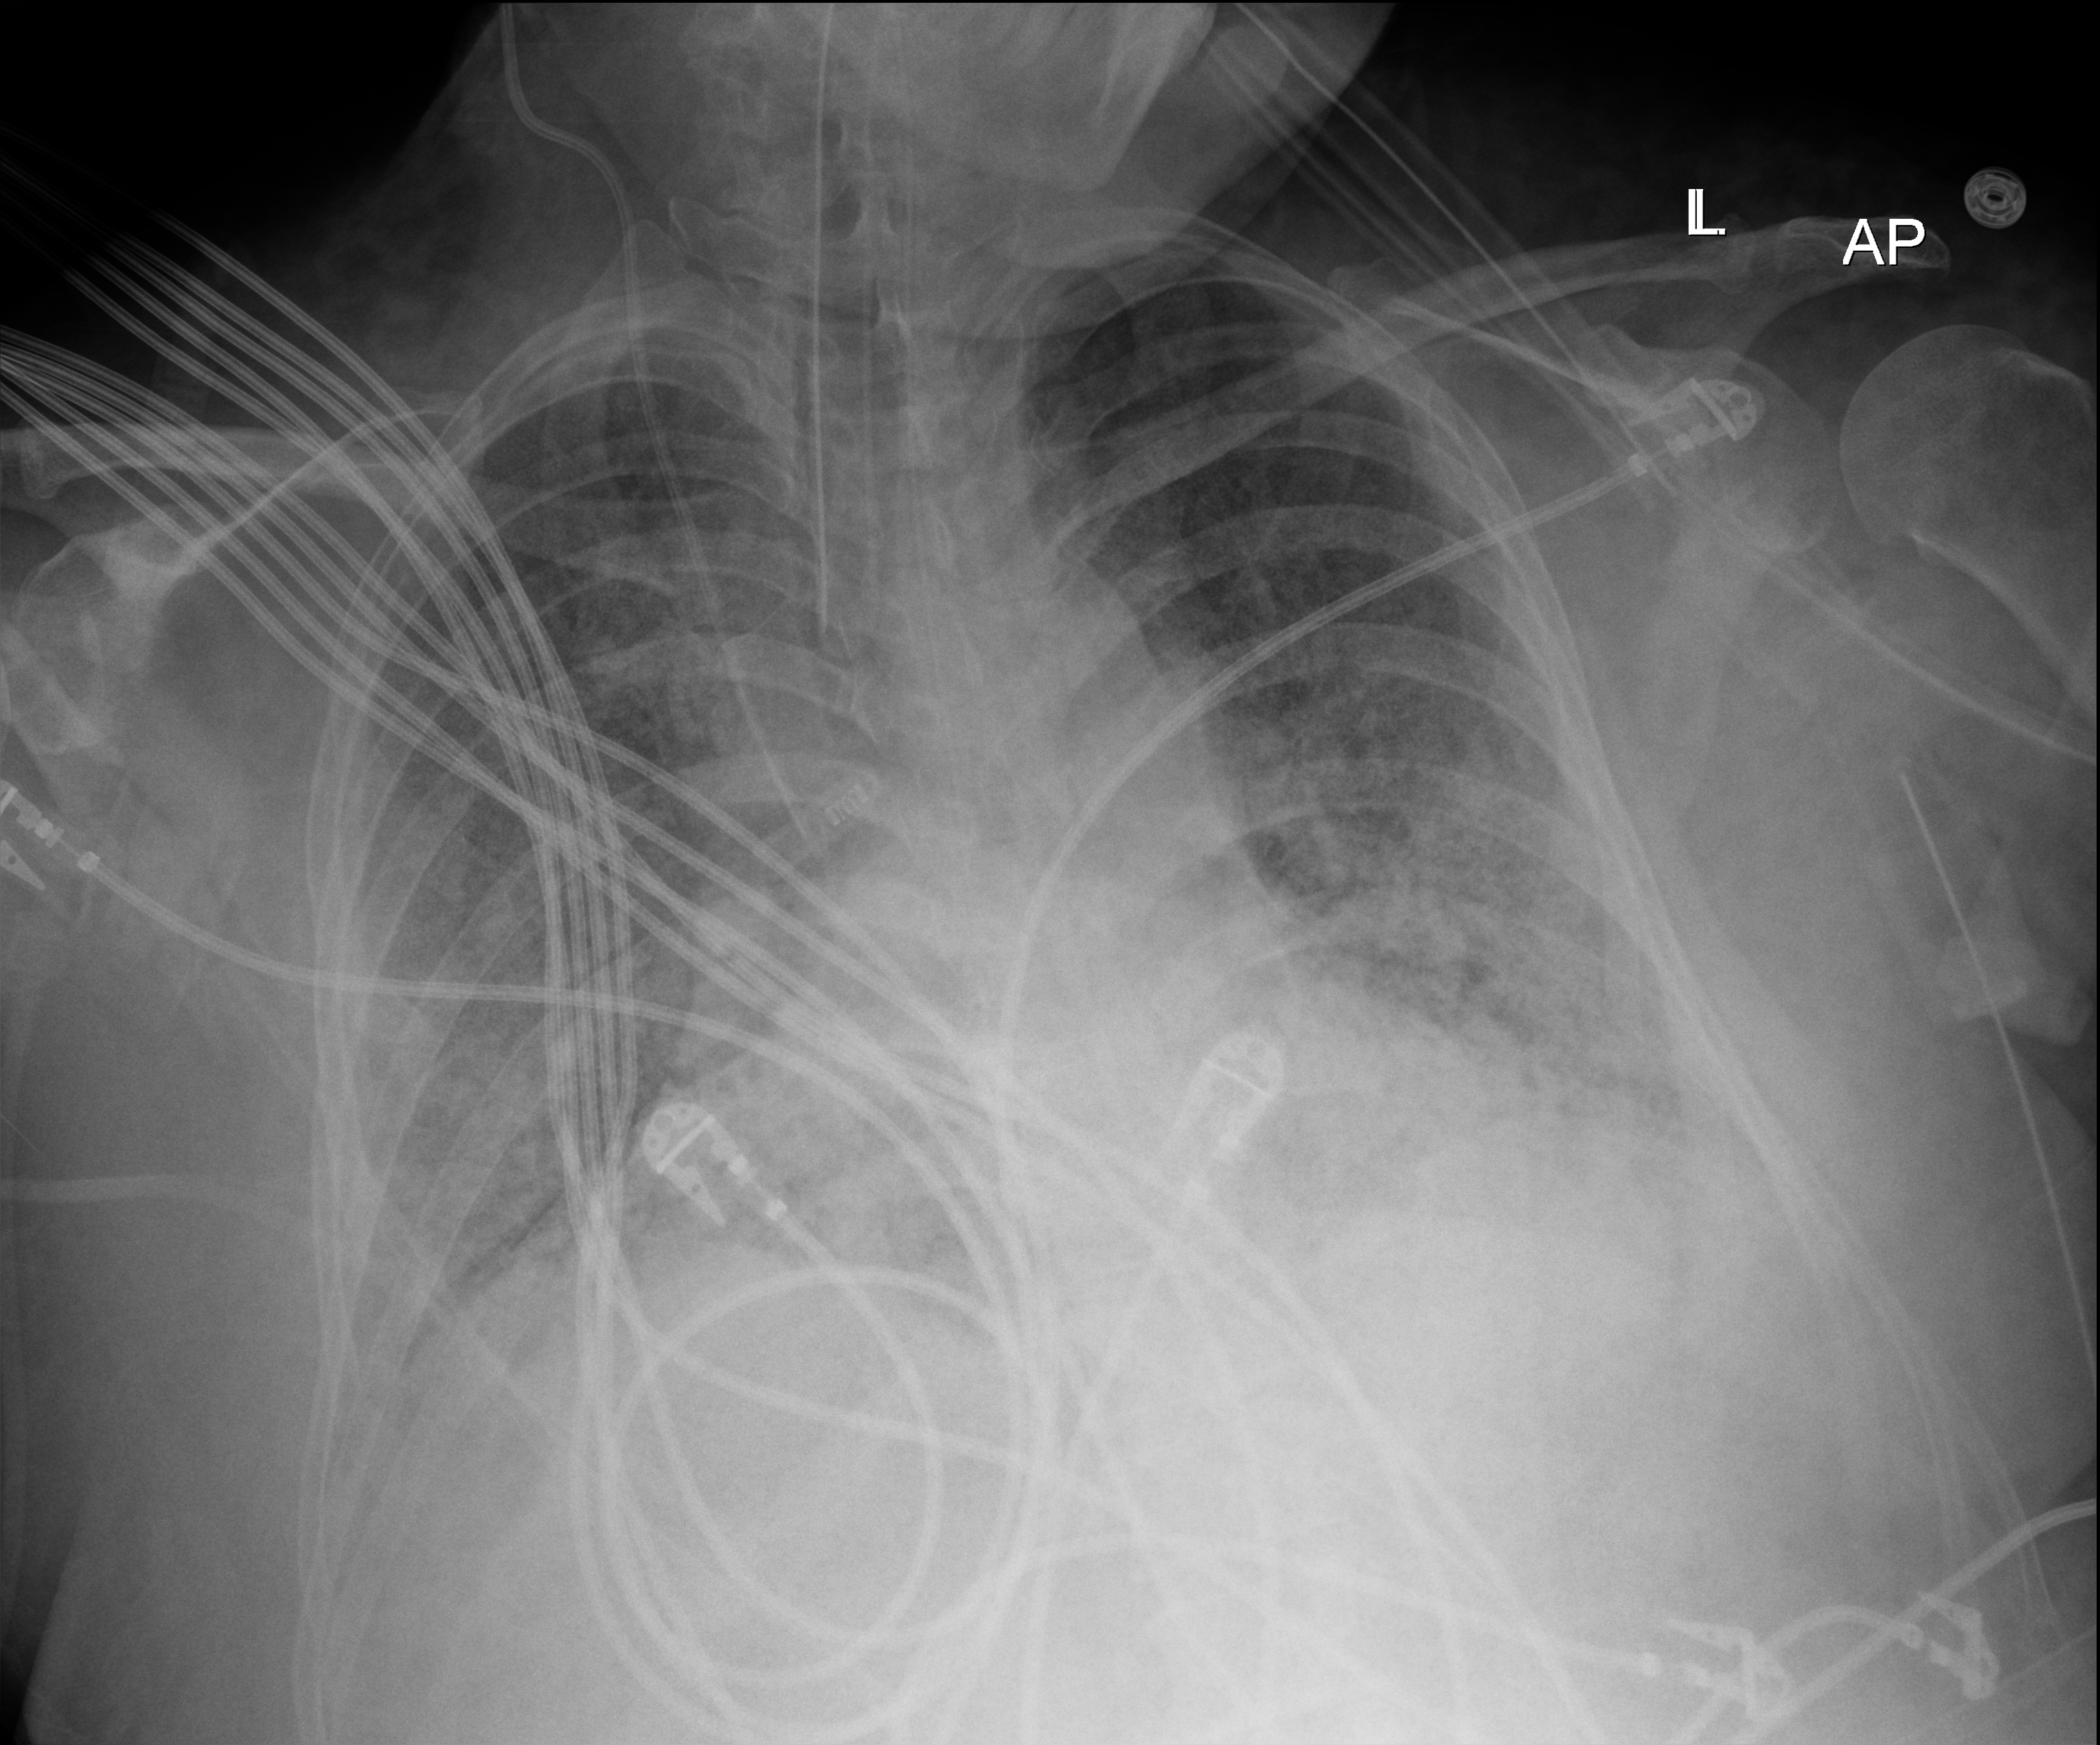
Chest X-ray (portable); anteroposterior (AP) projection. Adult patient hospitalised with COVID-19, age 18–59 years.
Hospital-stay facts (about this admission, not read from this image; timing relative to this image not recorded): diabetes (admission record): no.